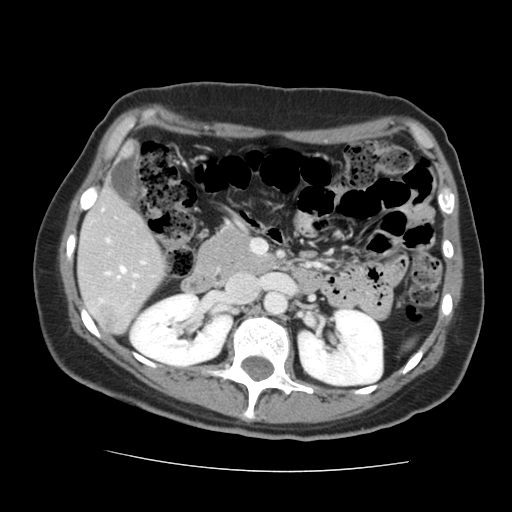
Contrast-enhanced abdominal CT, one axial slice. Intravenous contrast given. Soft-tissue window (W 400 / L 40 HU). 2.5 mm slice thickness. 512 × 512 image matrix. Female patient, age 46 years. From the clinical record (not read from this slice): diagnosis: colorectal cancer liver metastases, imaged before liver resection; multiple liver metastases: no; largest metastasis: 2.8 cm; disease in both lobes: no.
Structures marked on this image (manually delineated by an expert):
- liver: box from (x=79, y=191) to (x=165, y=333) px
- planned liver remnant (the part of the liver to remain after resection): (x=79, y=191)–(x=165, y=333)
- portal vein (with intrahepatic branches): (x=106, y=239)–(x=144, y=279)
- liver metastasis: (x=102, y=306)–(x=115, y=329)